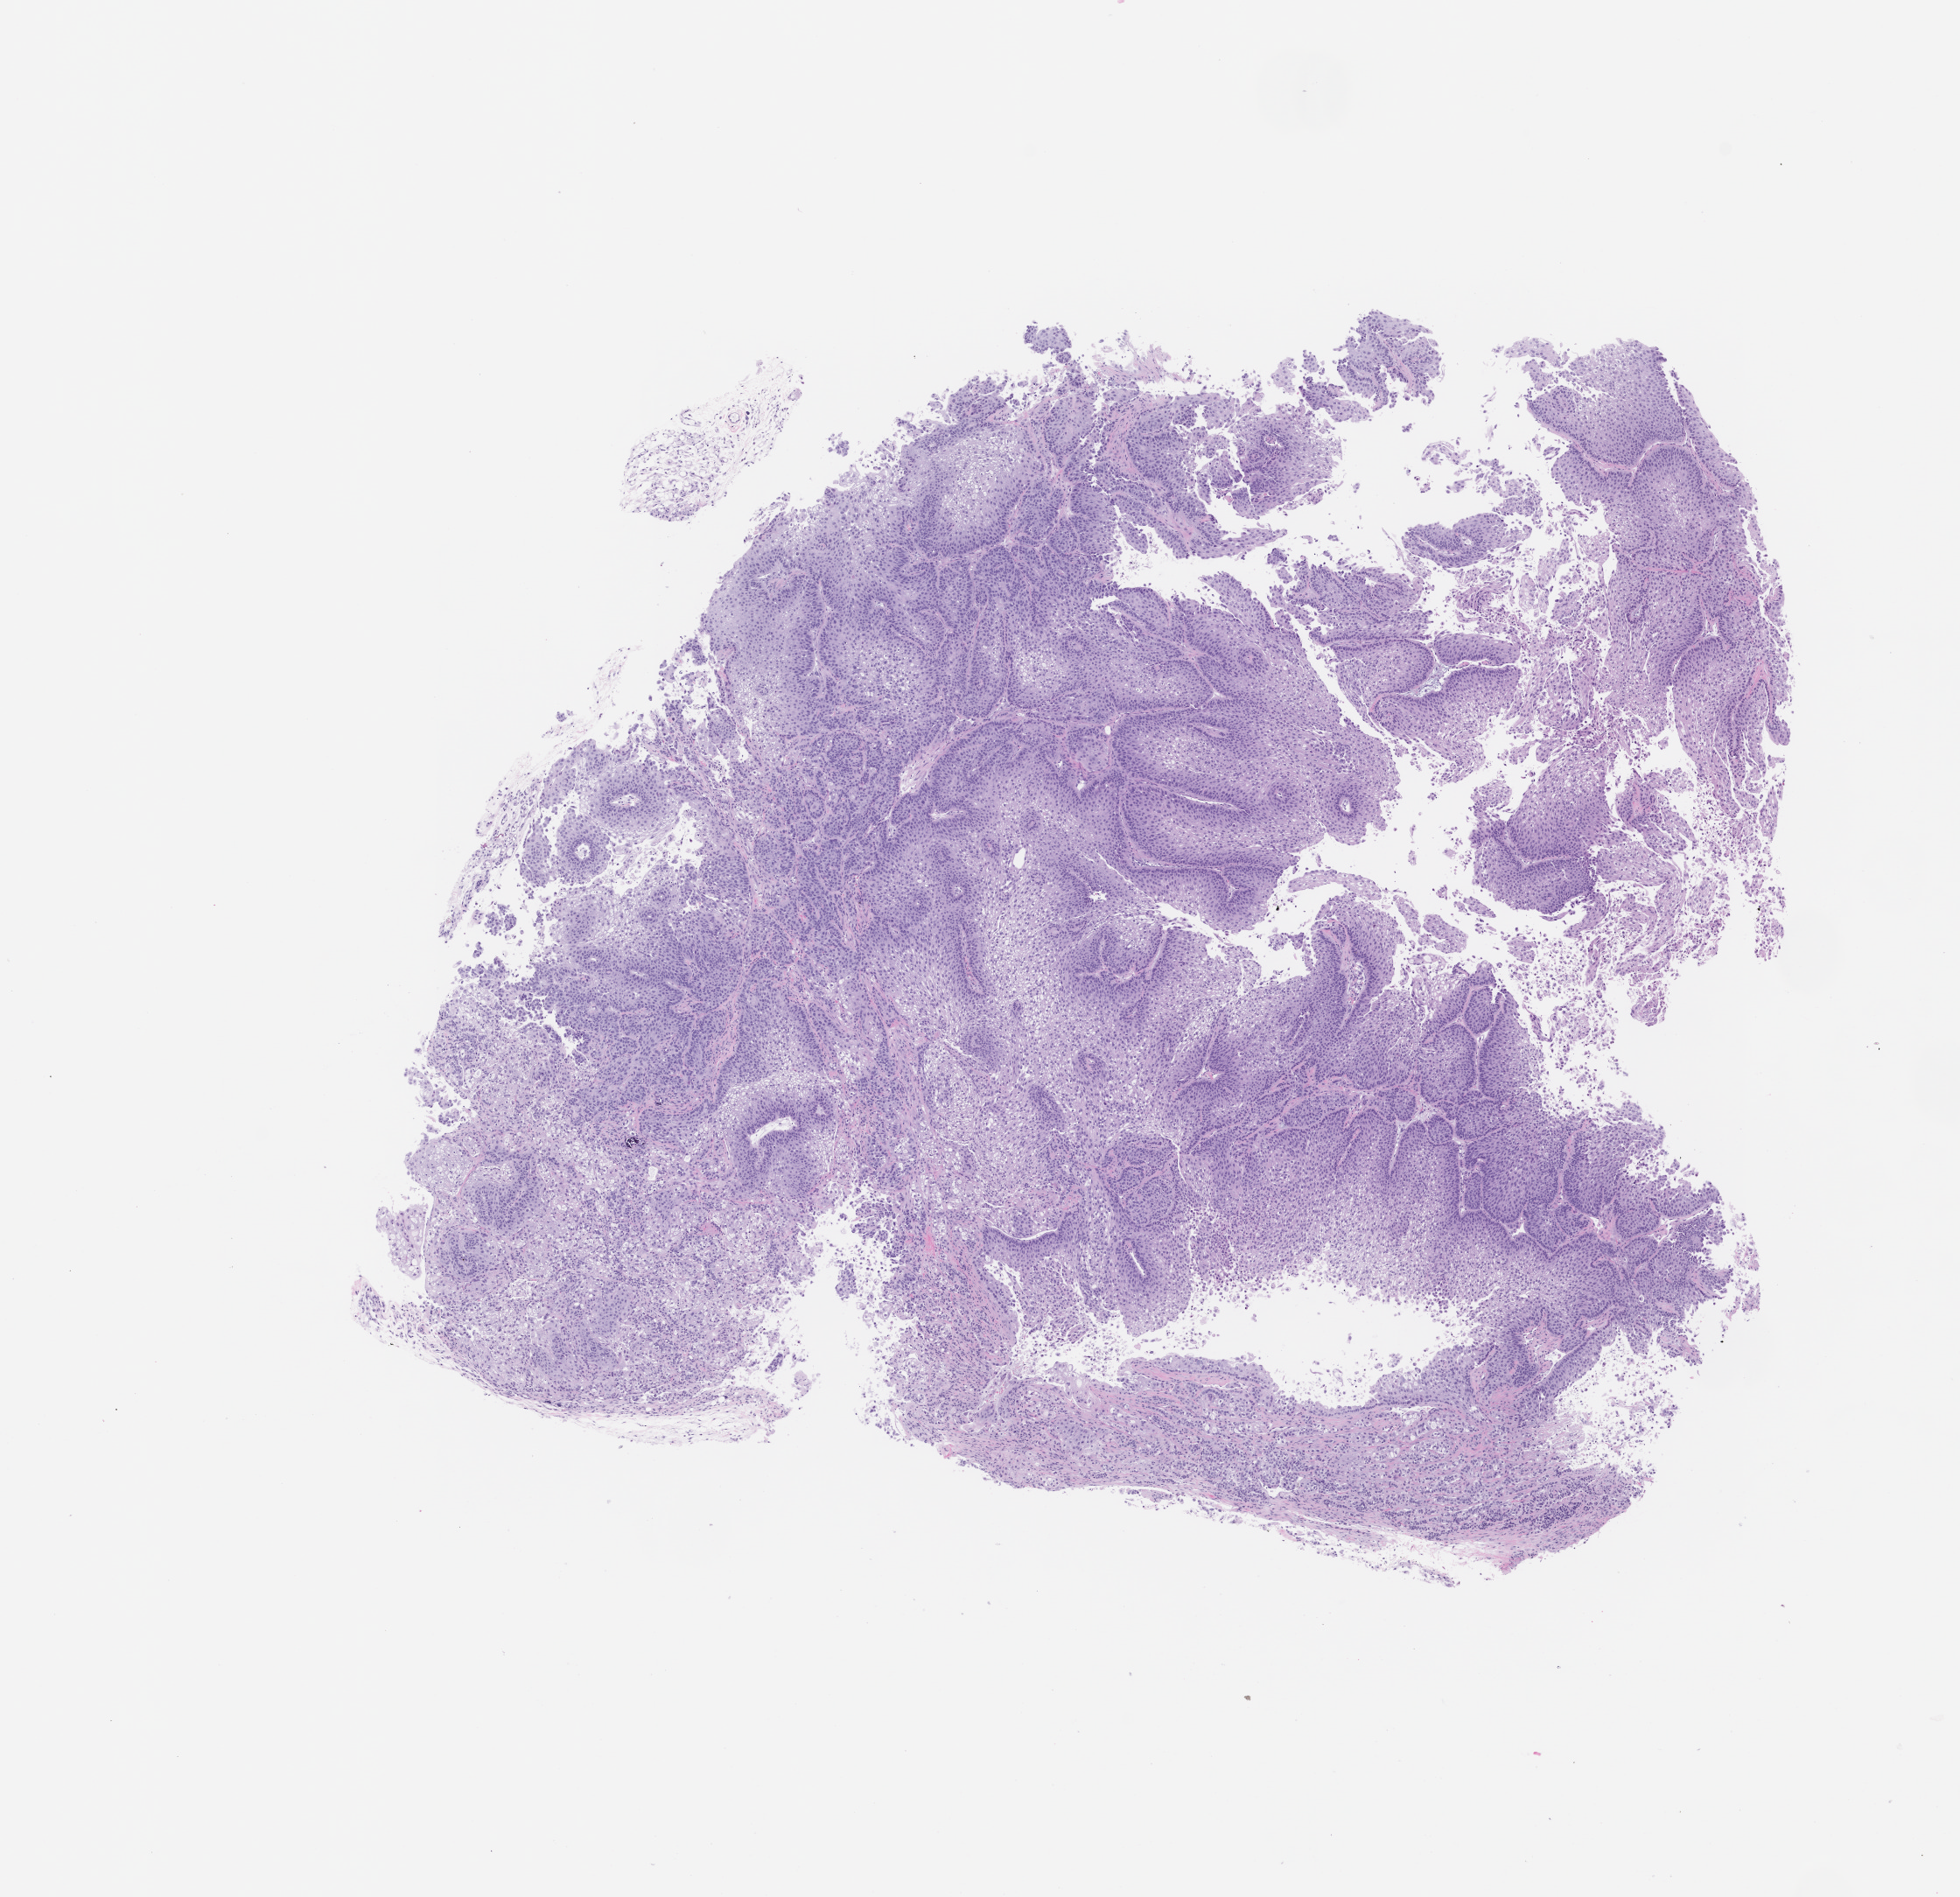
H&E whole-slide image of a patient-derived xenograft (PDX) tumor grown in a mouse, passage 2 — shown as a low-resolution overview of the whole scanned area (about 9.0 x 8.7 mm); formalin-fixed paraffin-embedded section; originating tumor site category: bladder.
* originating patient diagnosis: Urothelial Carcinoma